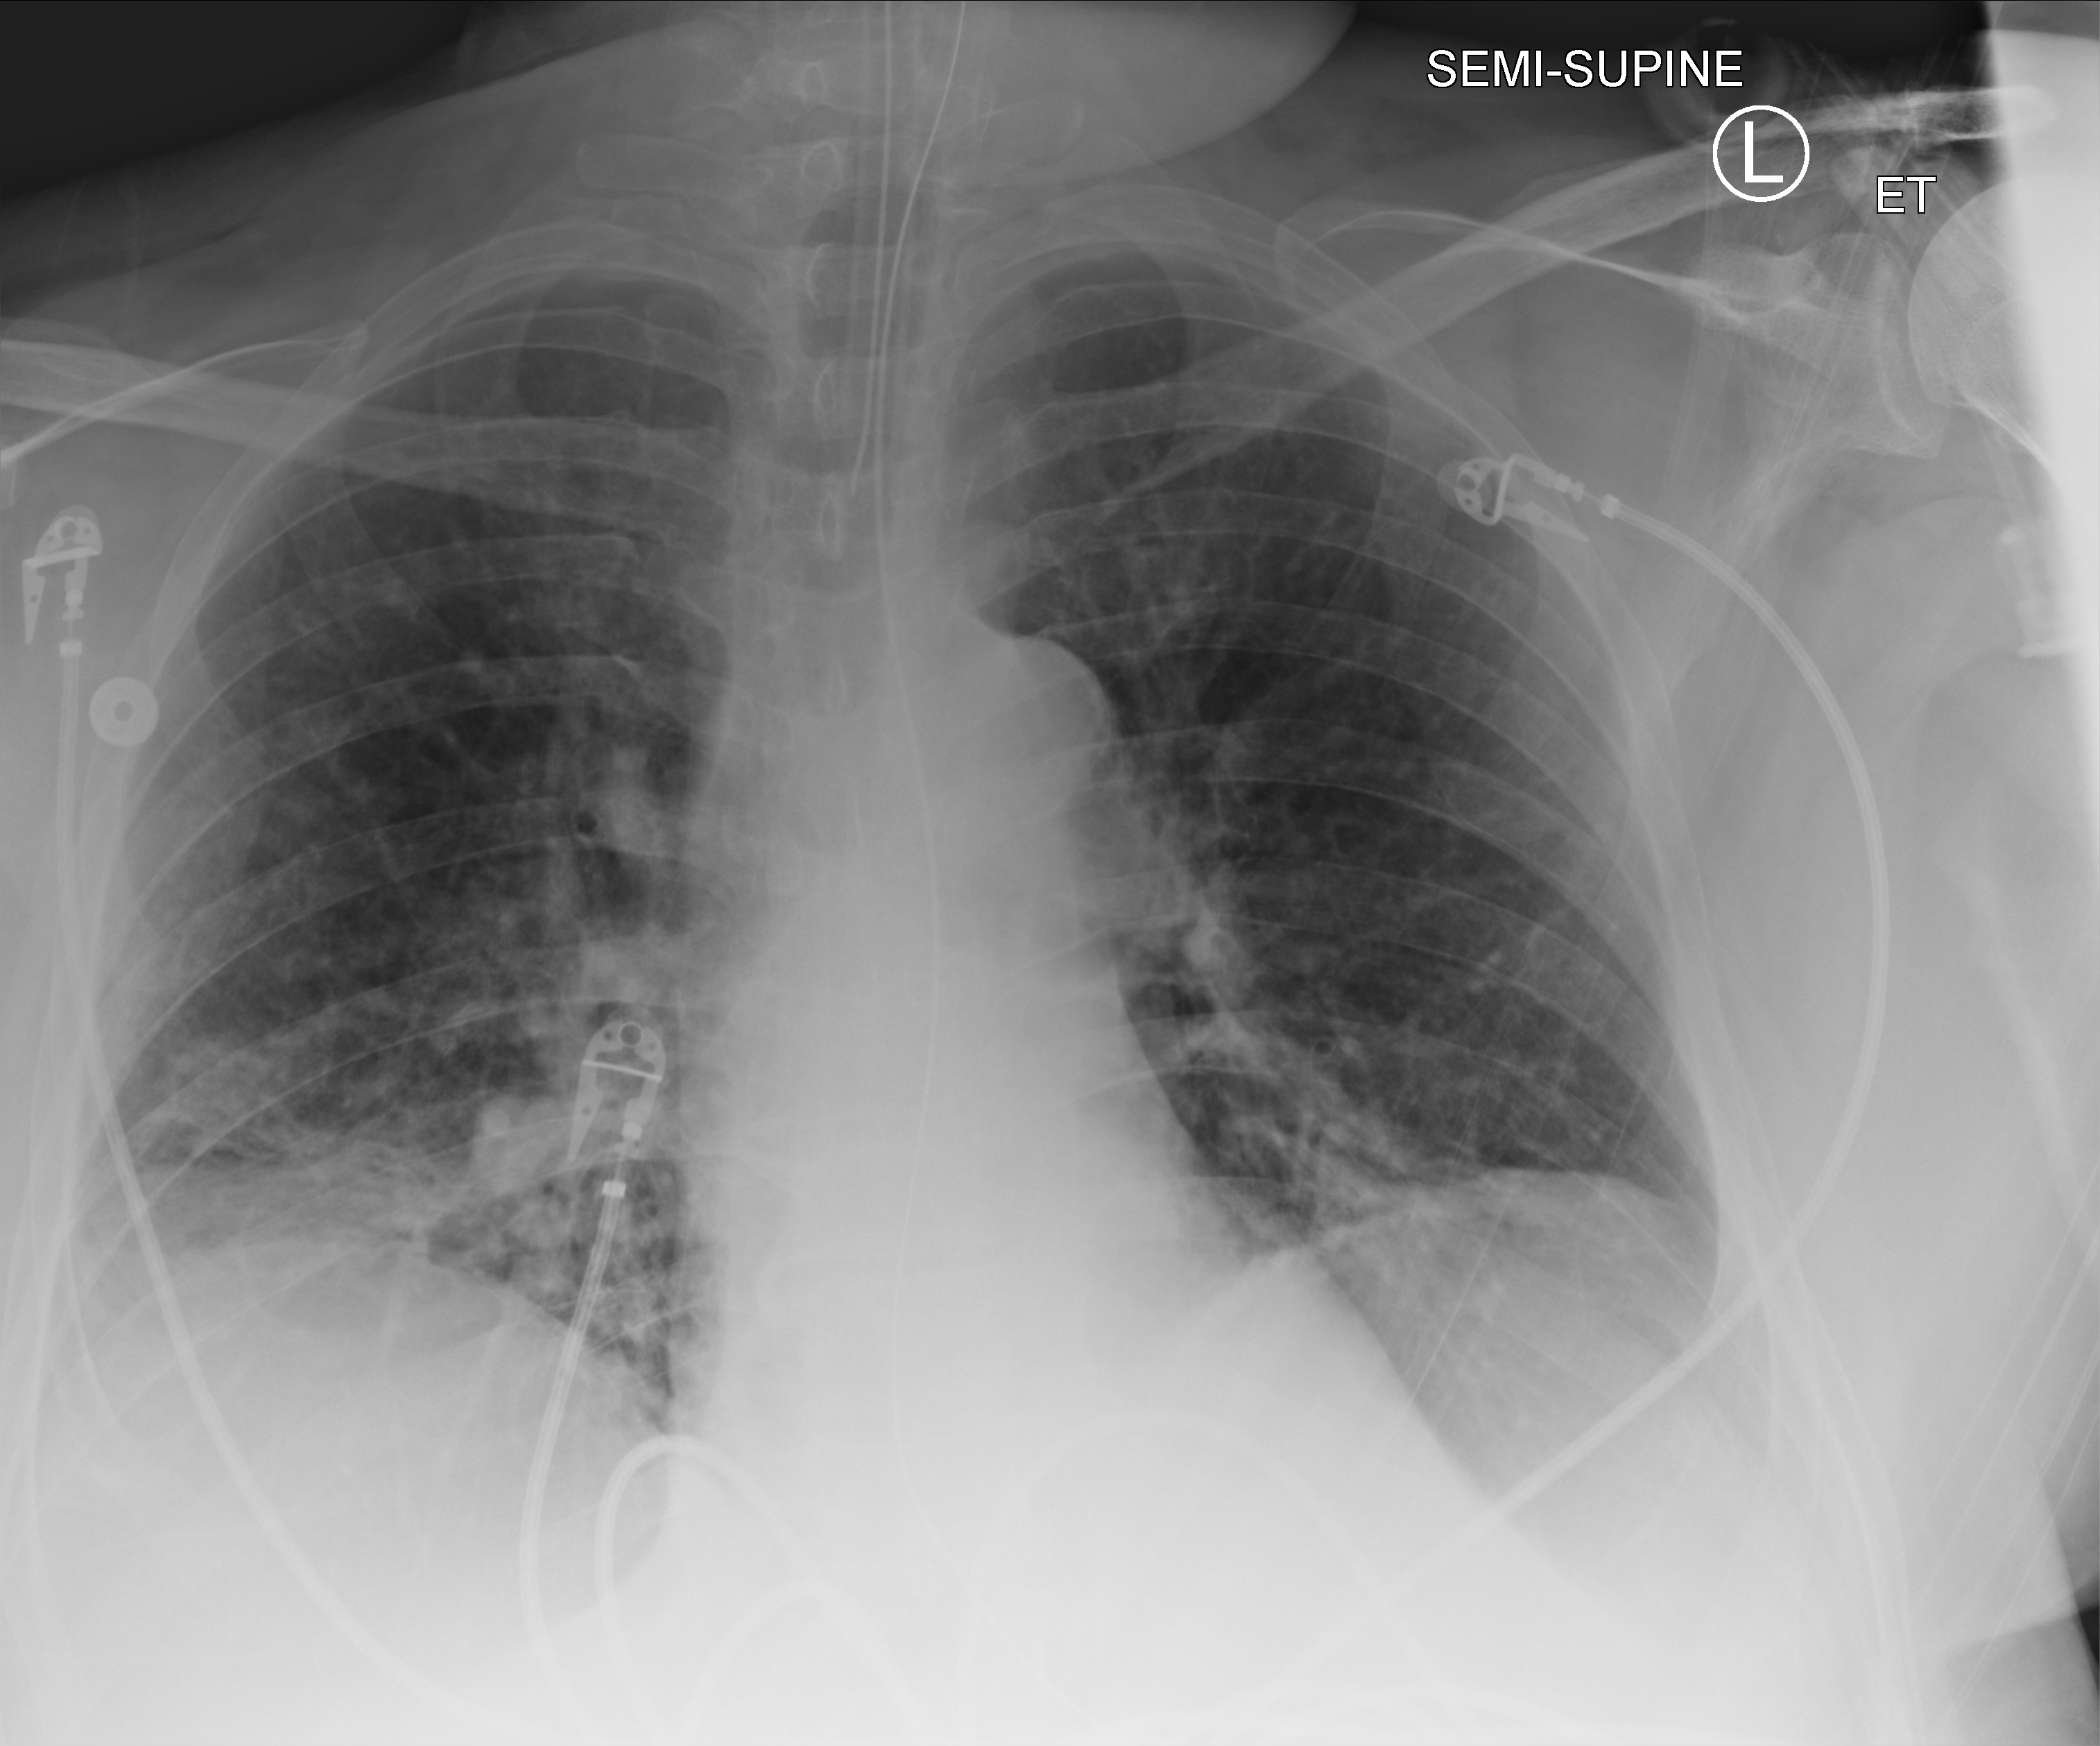
Chest X-ray (portable), anteroposterior (AP) projection. Male patient hospitalised with COVID-19, age 60–74 years.
Admission-level facts for this patient (not findings on this image; timing relative to this image not recorded):
- chronic kidney disease (admission record): no